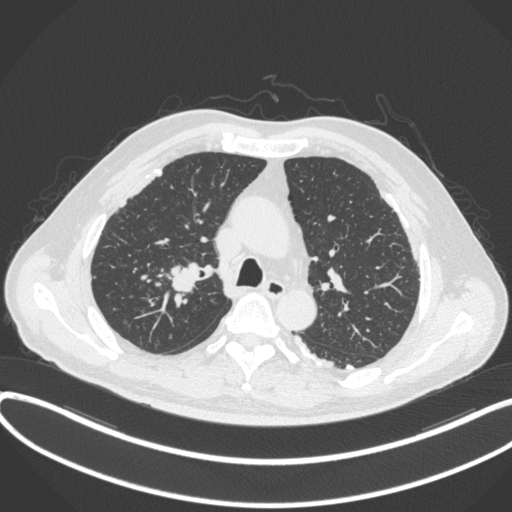
Chest CT, one axial slice; slice 292 of 455 in the series (ordered by position); reconstruction kernel B31f; 120 kVp; lung window (W 1500 / L -600 HU); 512 × 512 image matrix. Patient: male, 58 years. From the clinical record (not read from this slice): clinical TNM (as recorded): T1c N0 M0.
Structures marked on this image (rectangle marked by the reading radiologist):
- lung tumour (recorded histology: squamous cell carcinoma): bounding box (x1, y1, x2, y2) in pixels: (165, 259, 205, 294)